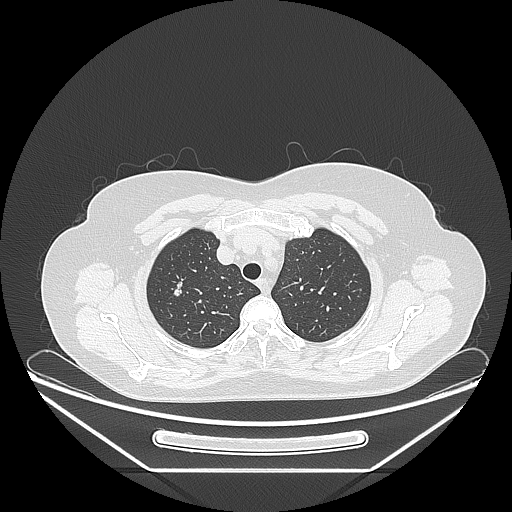
Chest CT, one axial slice; position 201 of 236 along the scan axis; reconstruction kernel LUNG; lung window (W 1500 / L -600 HU); 512 × 512 image matrix, field of view 433 × 433 mm. Female patient, age 60 years. From the clinical record (not read from this slice): clinical TNM (as recorded): T1c N0 M0; histopathological grade: G2-3.
Structures marked on this image (bounding box drawn by a radiologist):
- lung tumour (recorded histology: adenocarcinoma): bounding box (x1, y1, x2, y2) in pixels: (167, 274, 192, 304)